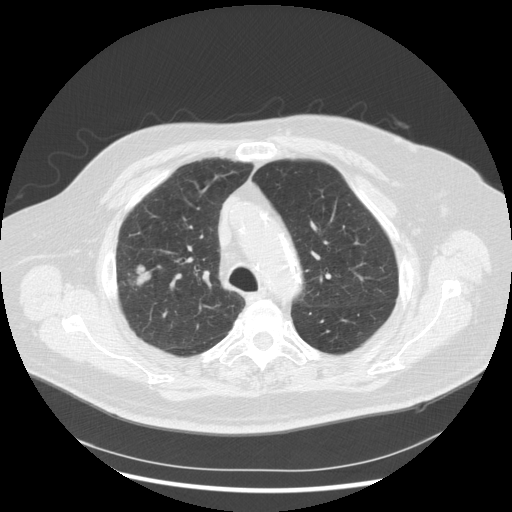
Low-dose screening chest CT, axial slice. Third screening round (two years after baseline). Lung window (W 1500 / L -600 HU). Standard (soft-tissue) reconstruction kernel (STANDARD). Slice 206 of 263 in the series. 512 × 512 image matrix. Male participant, aged 72 years at enrolment. Former smoker at enrolment.
Expert reader's lesion annotation, bounding box <112,252,164,302> (left, top, right, bottom; pixels). Screening reader's record for this exam (one nodule recorded; not confirmed to be the boxed lesion): non-calcified nodule or mass ≥4 mm, right upper lobe, 31 × 31 mm, poorly defined margins, soft tissue attenuation, pre-existing on the prior screen: no. Participant outcome: lung cancer diagnosed 70 days after this screen — squamous cell carcinoma, NOS, right upper lobe, poorly differentiated (G3), stage IIIA (AJCC 6th edition), 19 mm at pathology.